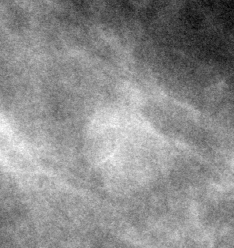
Cropped region of a digitized screen-film mammogram centred on a radiologist-marked abnormality, left breast, CC view.
- Marked abnormality: mass, shape lobulated, margins circumscribed; BI-RADS assessment category 3; subtlety rating 4 on a 1 (subtle) to 5 (obvious) scale; pathology (as recorded): benign.